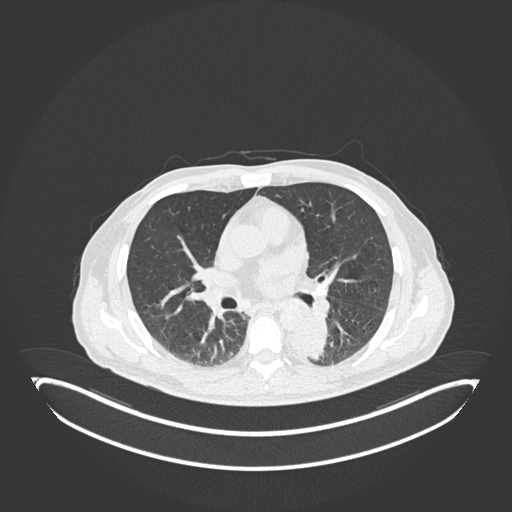
Chest CT, one axial slice. Position 107 of 251 along the scan axis. Reconstruction kernel B30f. 120 kVp. Lung window (W 1500 / L -600 HU). 512 × 512 image matrix. Male patient, age 72 years. Case-level facts recorded for this patient, not image findings: clinical TNM (as recorded): T2b N0 M1.
Structures marked on this image (bounding box drawn by a radiologist):
- lung tumour (recorded histology: adenocarcinoma): box from (x=287, y=316) to (x=330, y=361) px